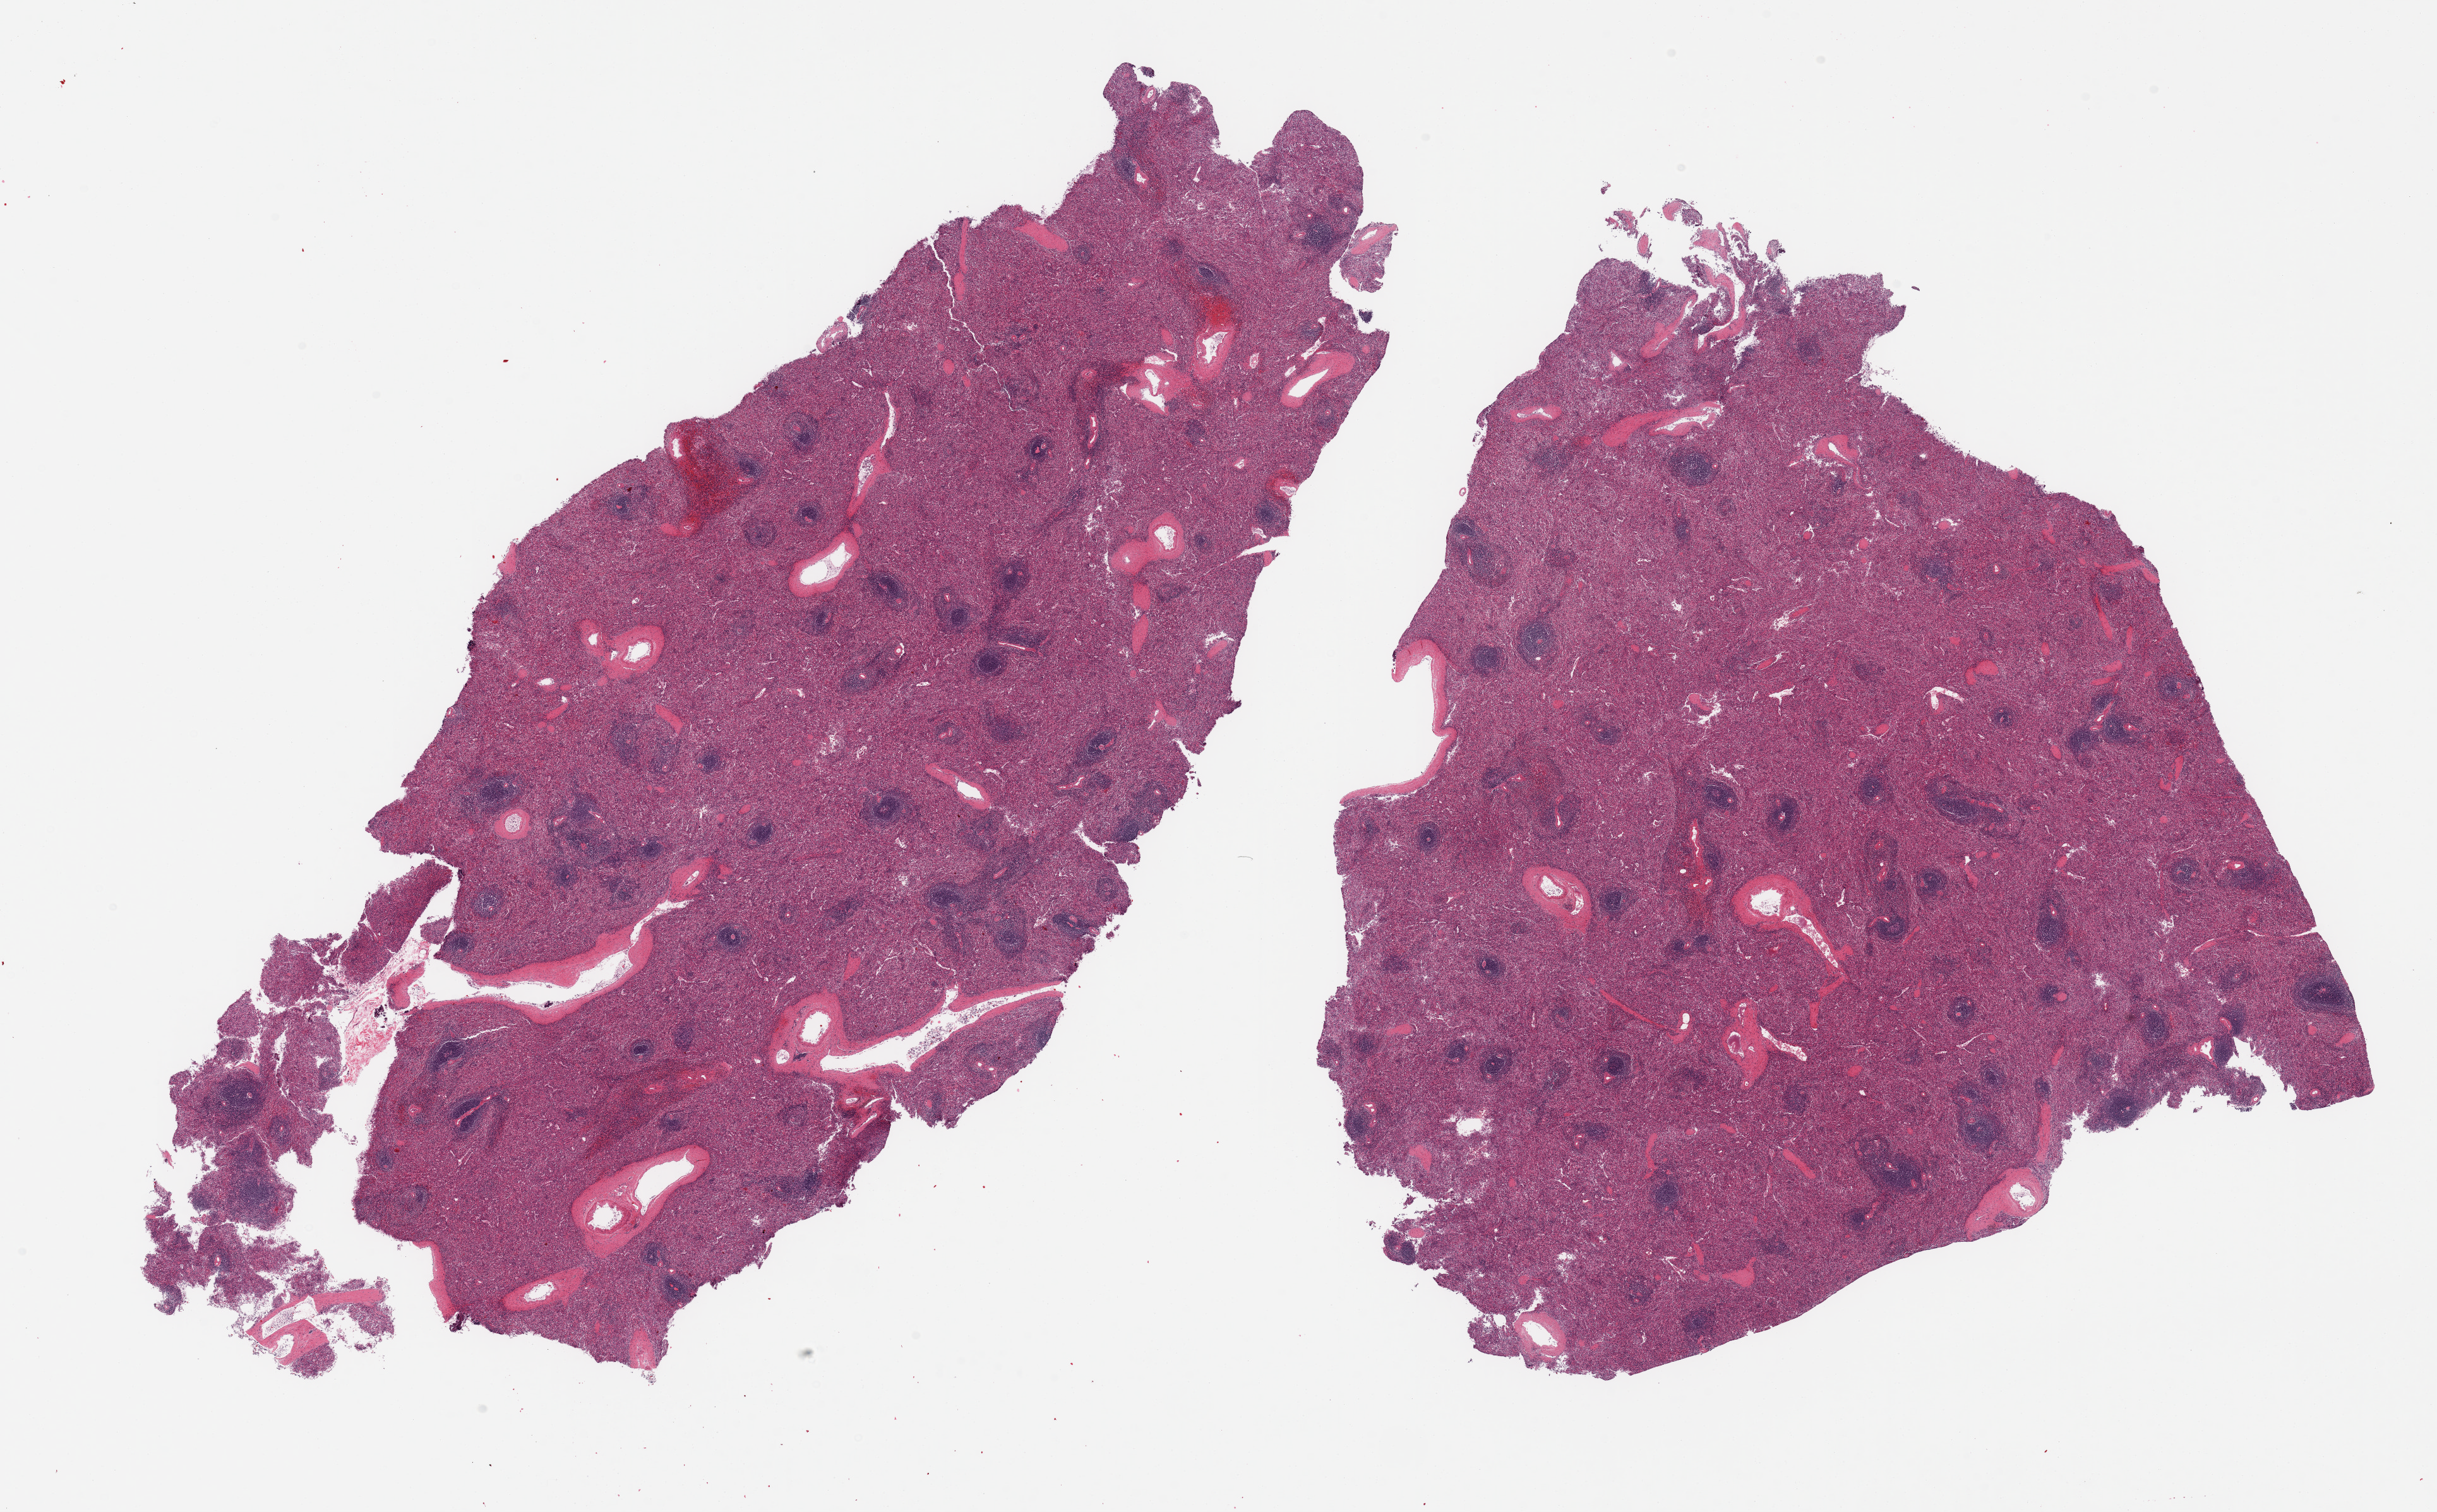
Whole-slide image, H&E stain, brightfield, a low-resolution overview of the entire scanned area, about 30.5 x 18.9 mm (acquisition: 20x scan). PAXgene-fixed, paraffin-embedded tissue. Target tissue: spleen. Donor tissue sample.
* reviewer comment on this tissue sample: 2 pieces, no abnormalities